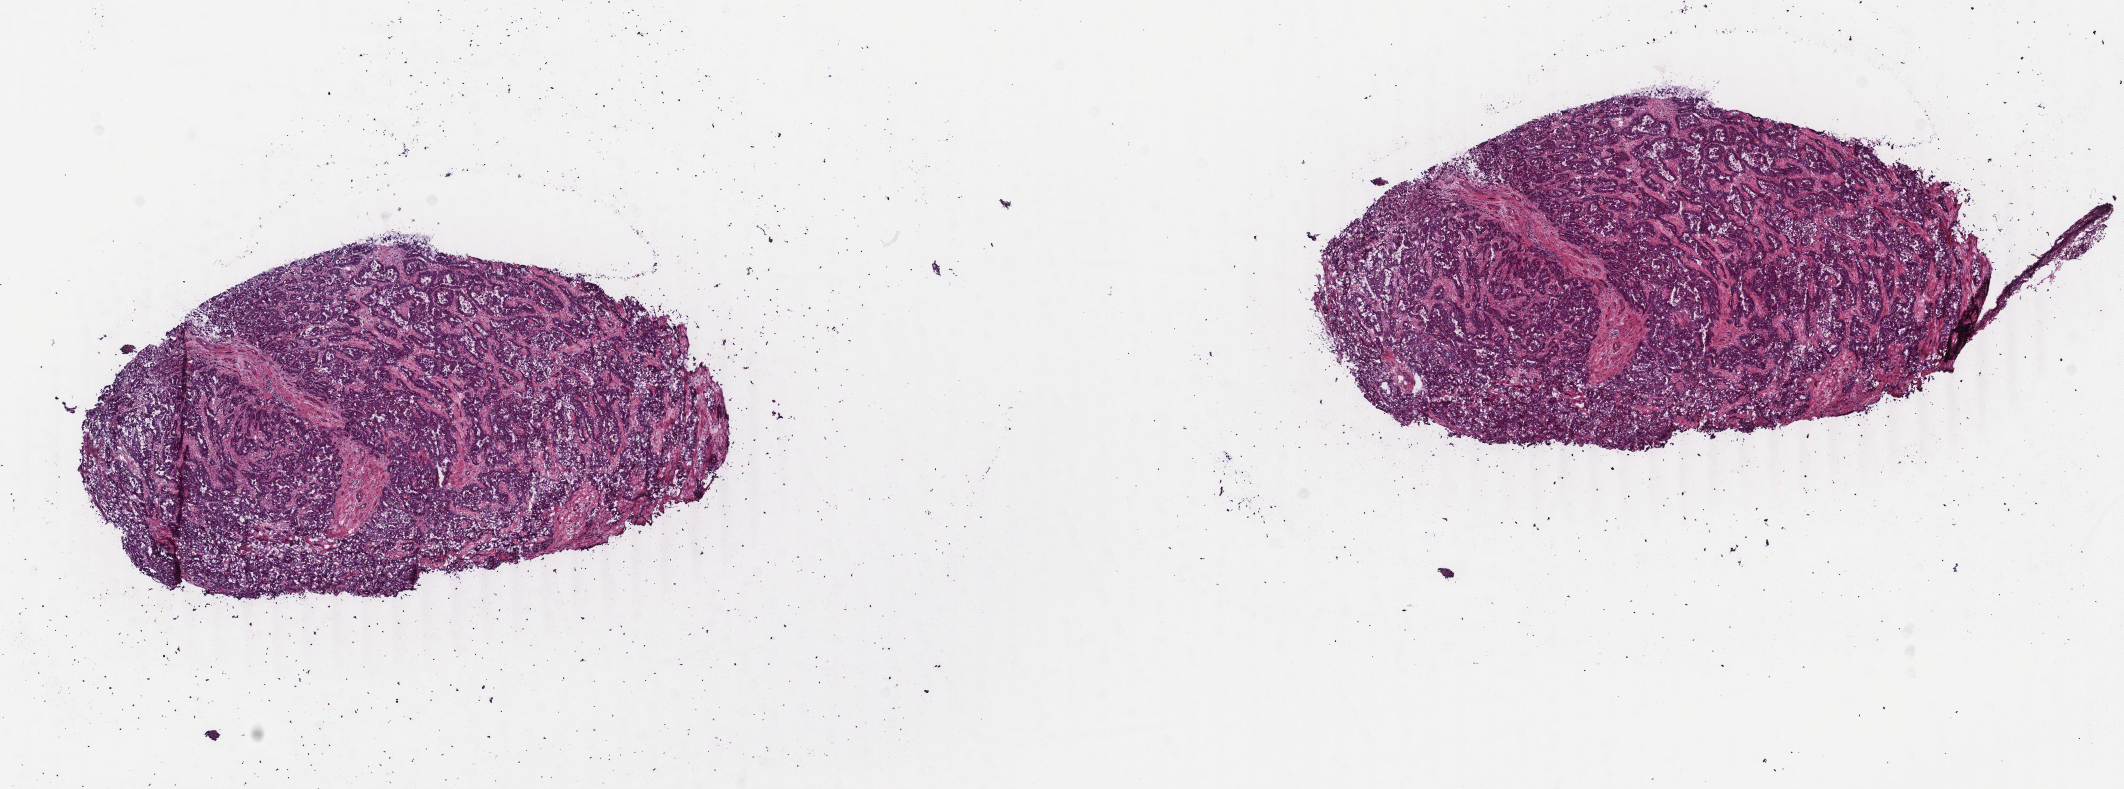
Whole-slide histology image, H&E-stained, whole scanned area (about 16.9 x 6.3 mm, acquisition: 40x scan) shown as a low-resolution overview; frozen section; primary tumour sample from the liver. Male patient; age at initial diagnosis 80 years. Histologic grade: G2 (moderately differentiated). Pathologist review of this section (percent, as recorded): tumour cells 70%, tumour nuclei 70%, normal cells 0%, stromal cells 30%, necrosis 0%. Infiltration values recorded for this section: lymphocyte infiltration 10%, monocyte infiltration 0%, neutrophil infiltration 0%.
Diagnosis: Hepatocellular carcinoma, NOS.